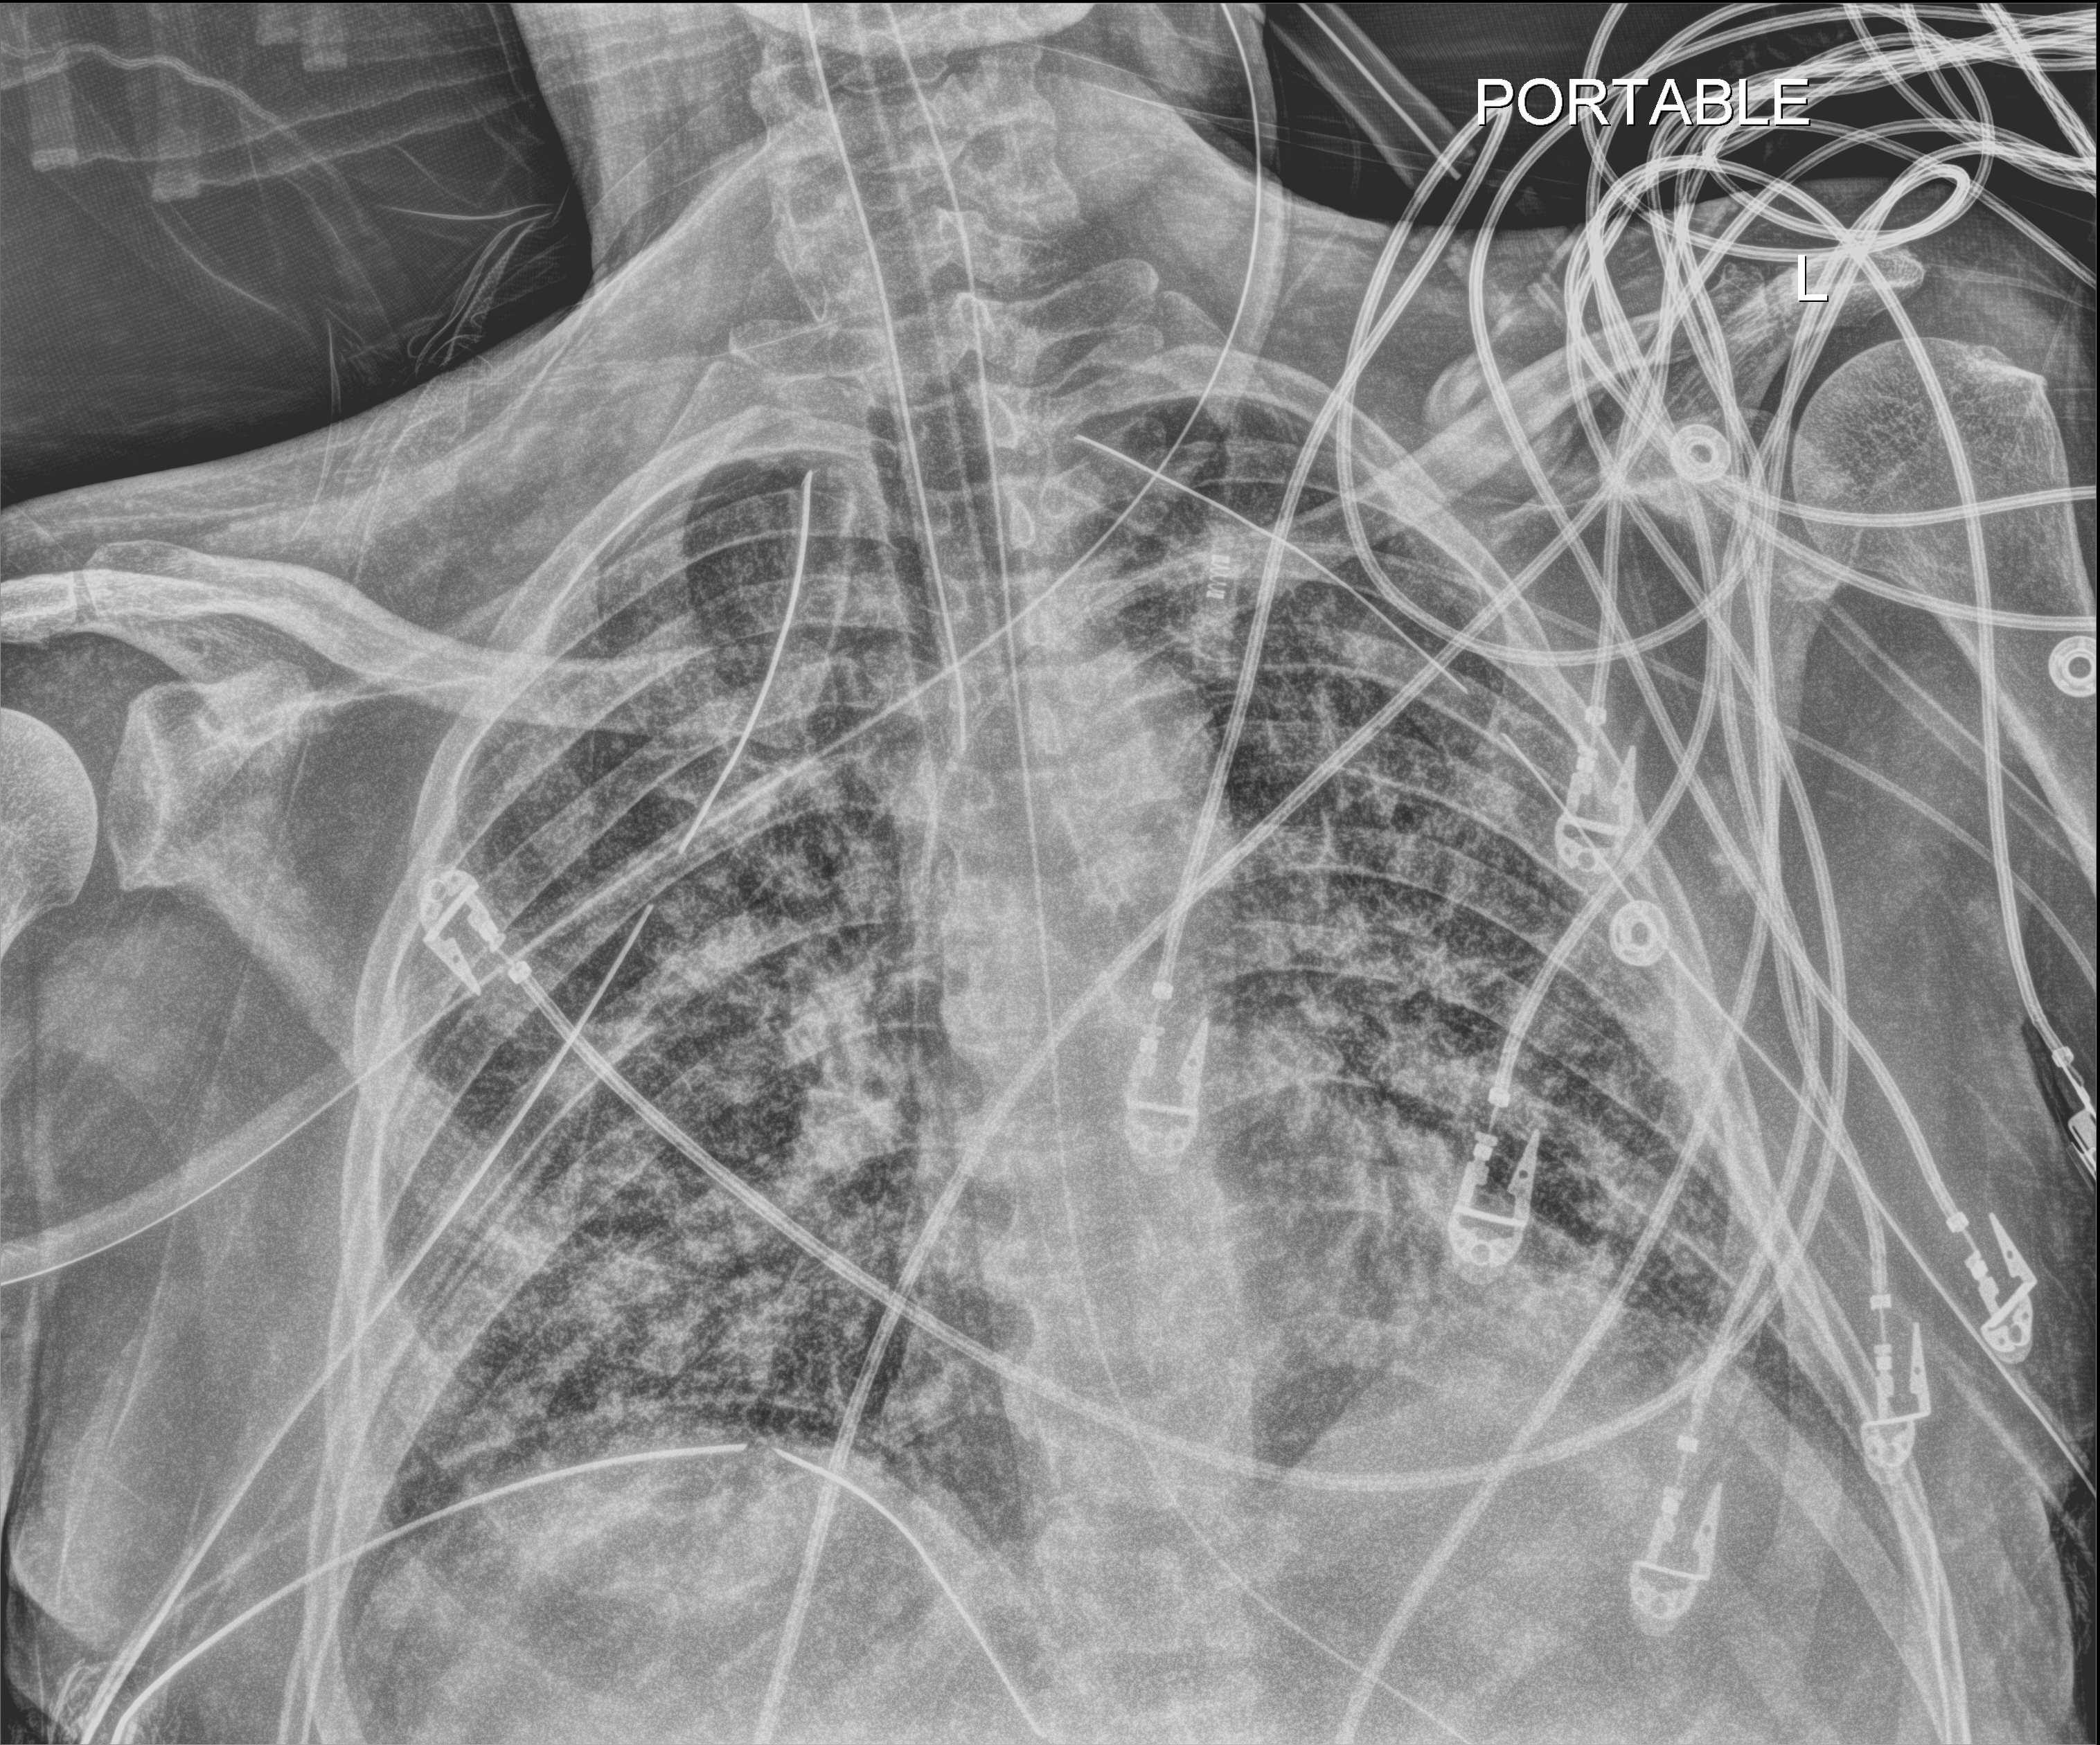
Bedside chest radiograph (digital radiography); anteroposterior (AP) projection. Male patient hospitalised with COVID-19, age 18–59 years.
Hospital-stay facts (about this admission, not read from this image; timing relative to this image not recorded): chronic kidney disease (admission record): no.